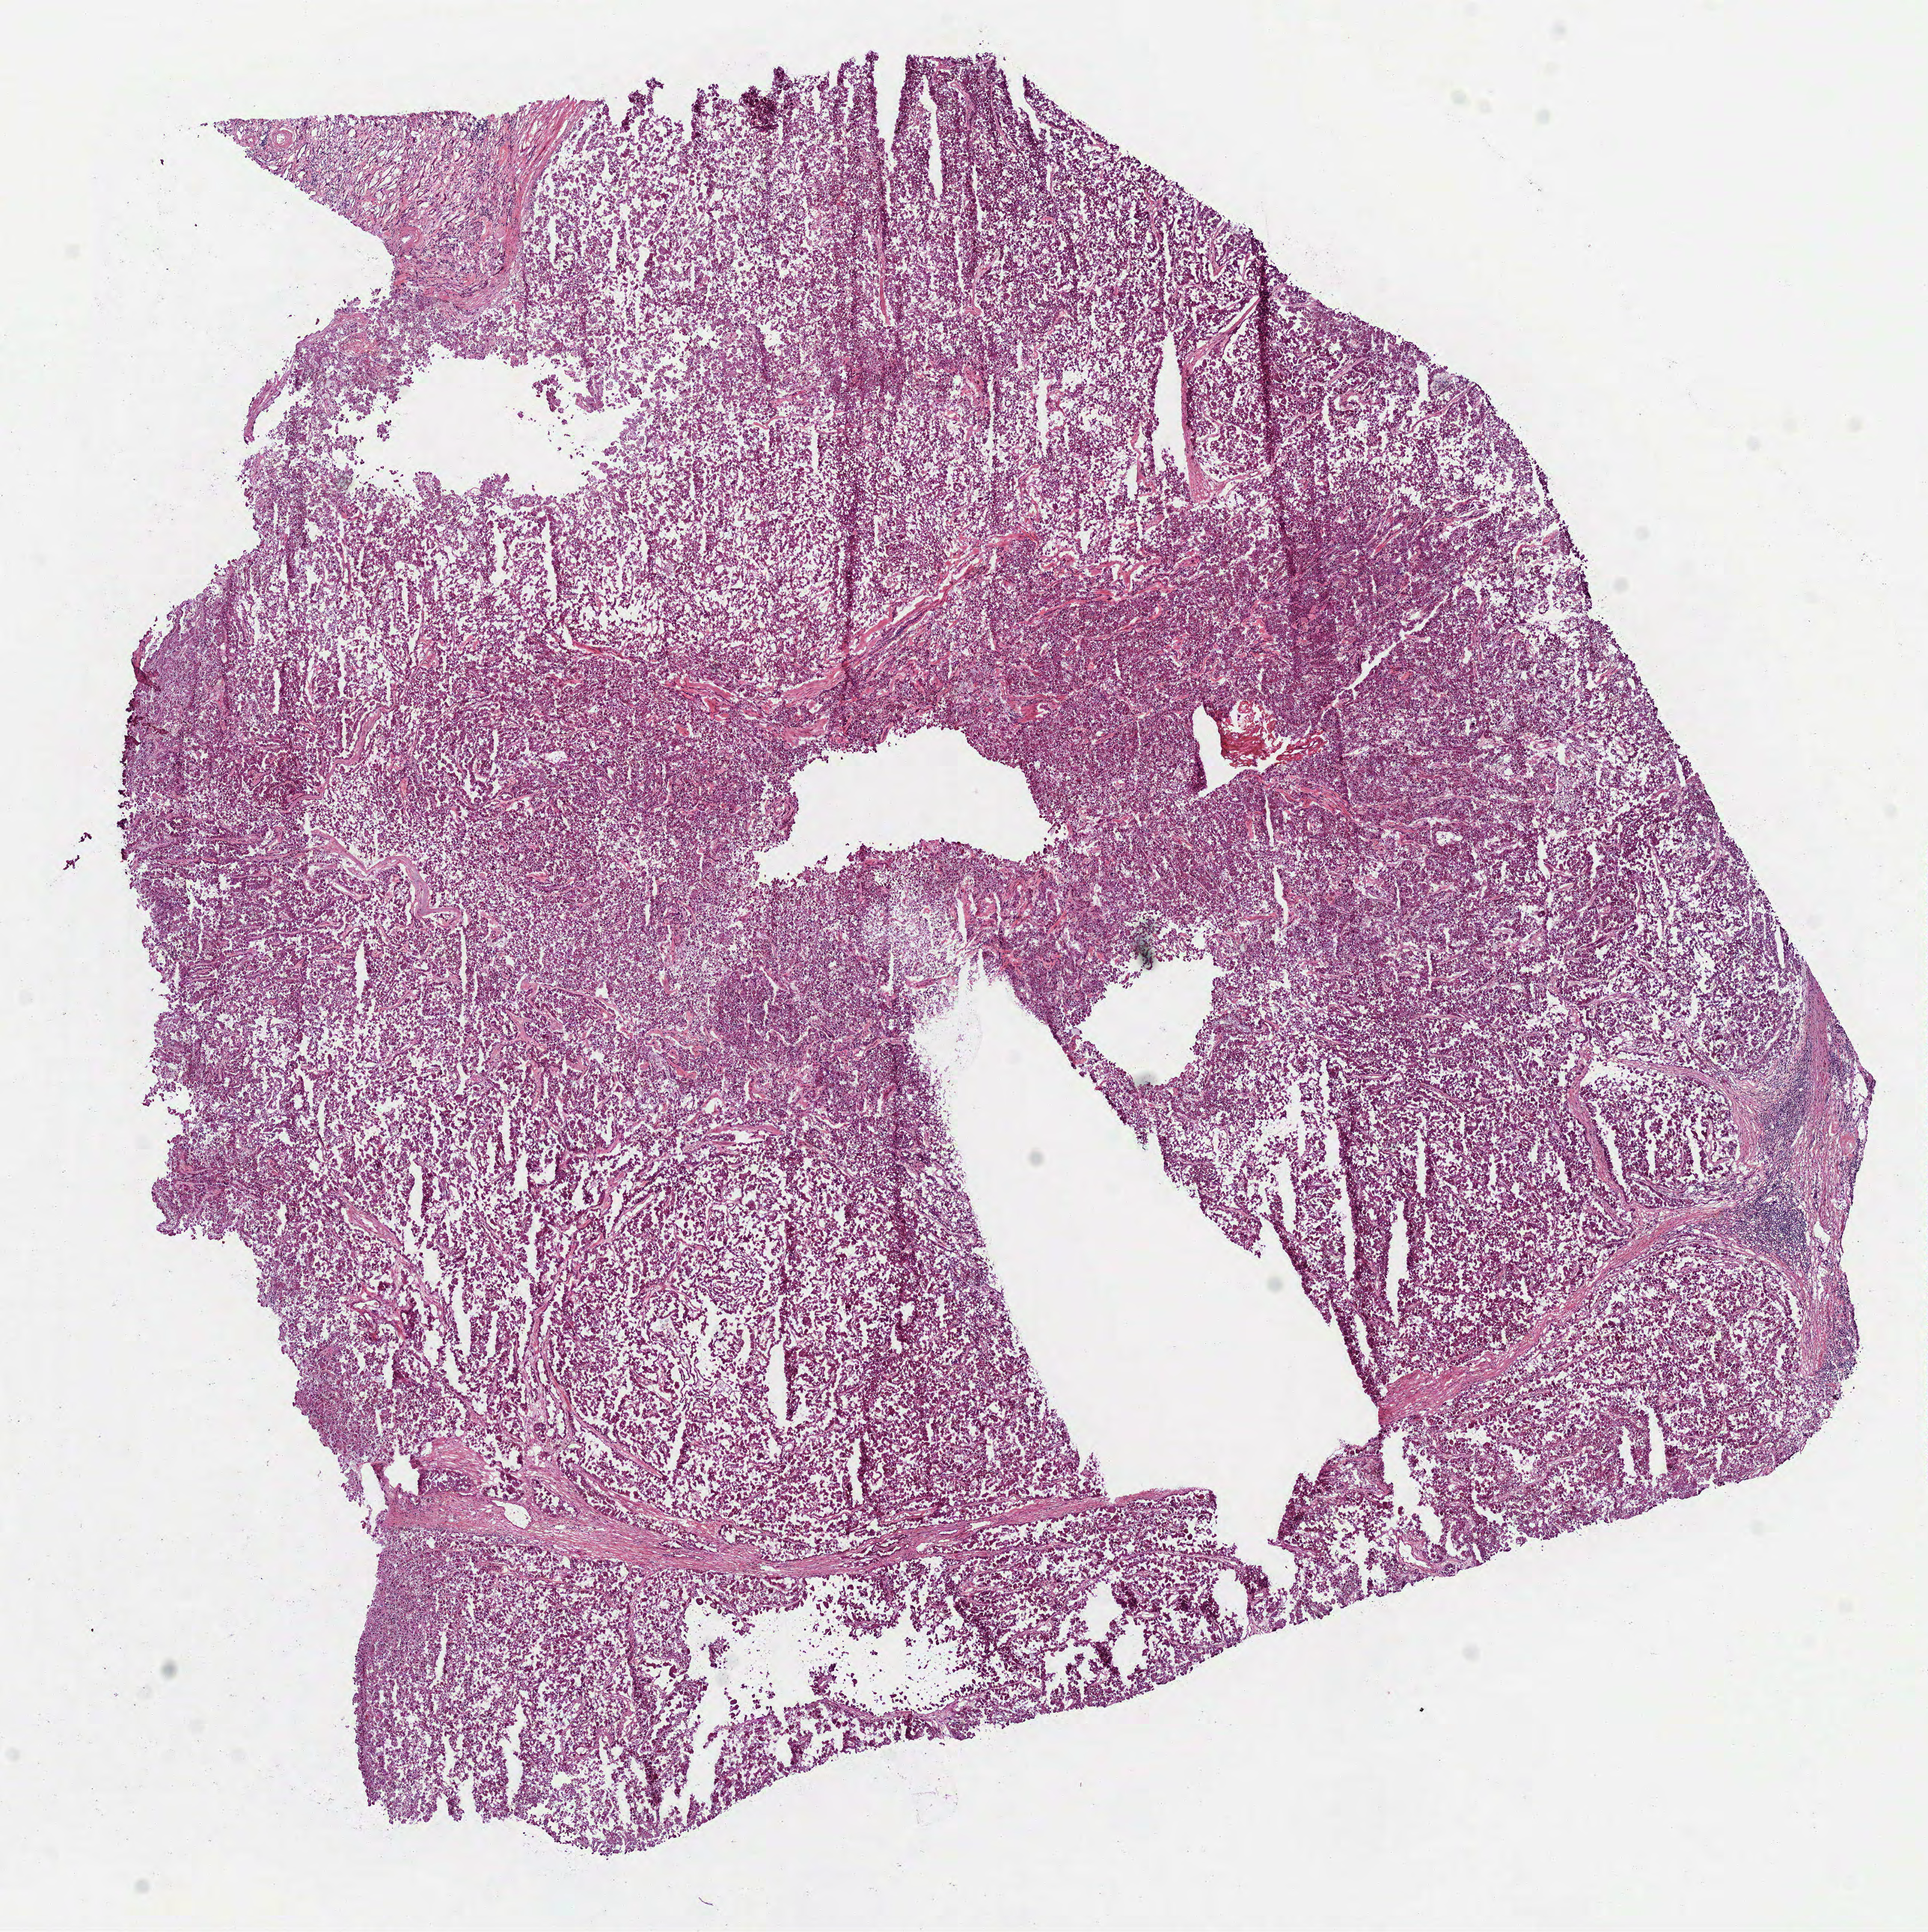
H&E whole-slide image, low-resolution overview of the scanned area, about 10.4 x 10.4 mm, frozen section from the bottom of the tissue portion, primary tumour sample from the kidney. Patient: male, age at initial diagnosis 81 years. Pathologist review of this section (percent, as recorded): tumour cells 100%, tumour nuclei 90%, normal cells 0%, stromal cells 0%, necrosis 0%. Inflammatory infiltration, as recorded: lymphocyte infiltration 5%, monocyte infiltration 0%, neutrophil infiltration 0%.
- lymph nodes positive (case pathology): 3 of 8 examined
- AJCC pathologic stage: III
- pathologic diagnosis: Papillary adenocarcinoma, NOS